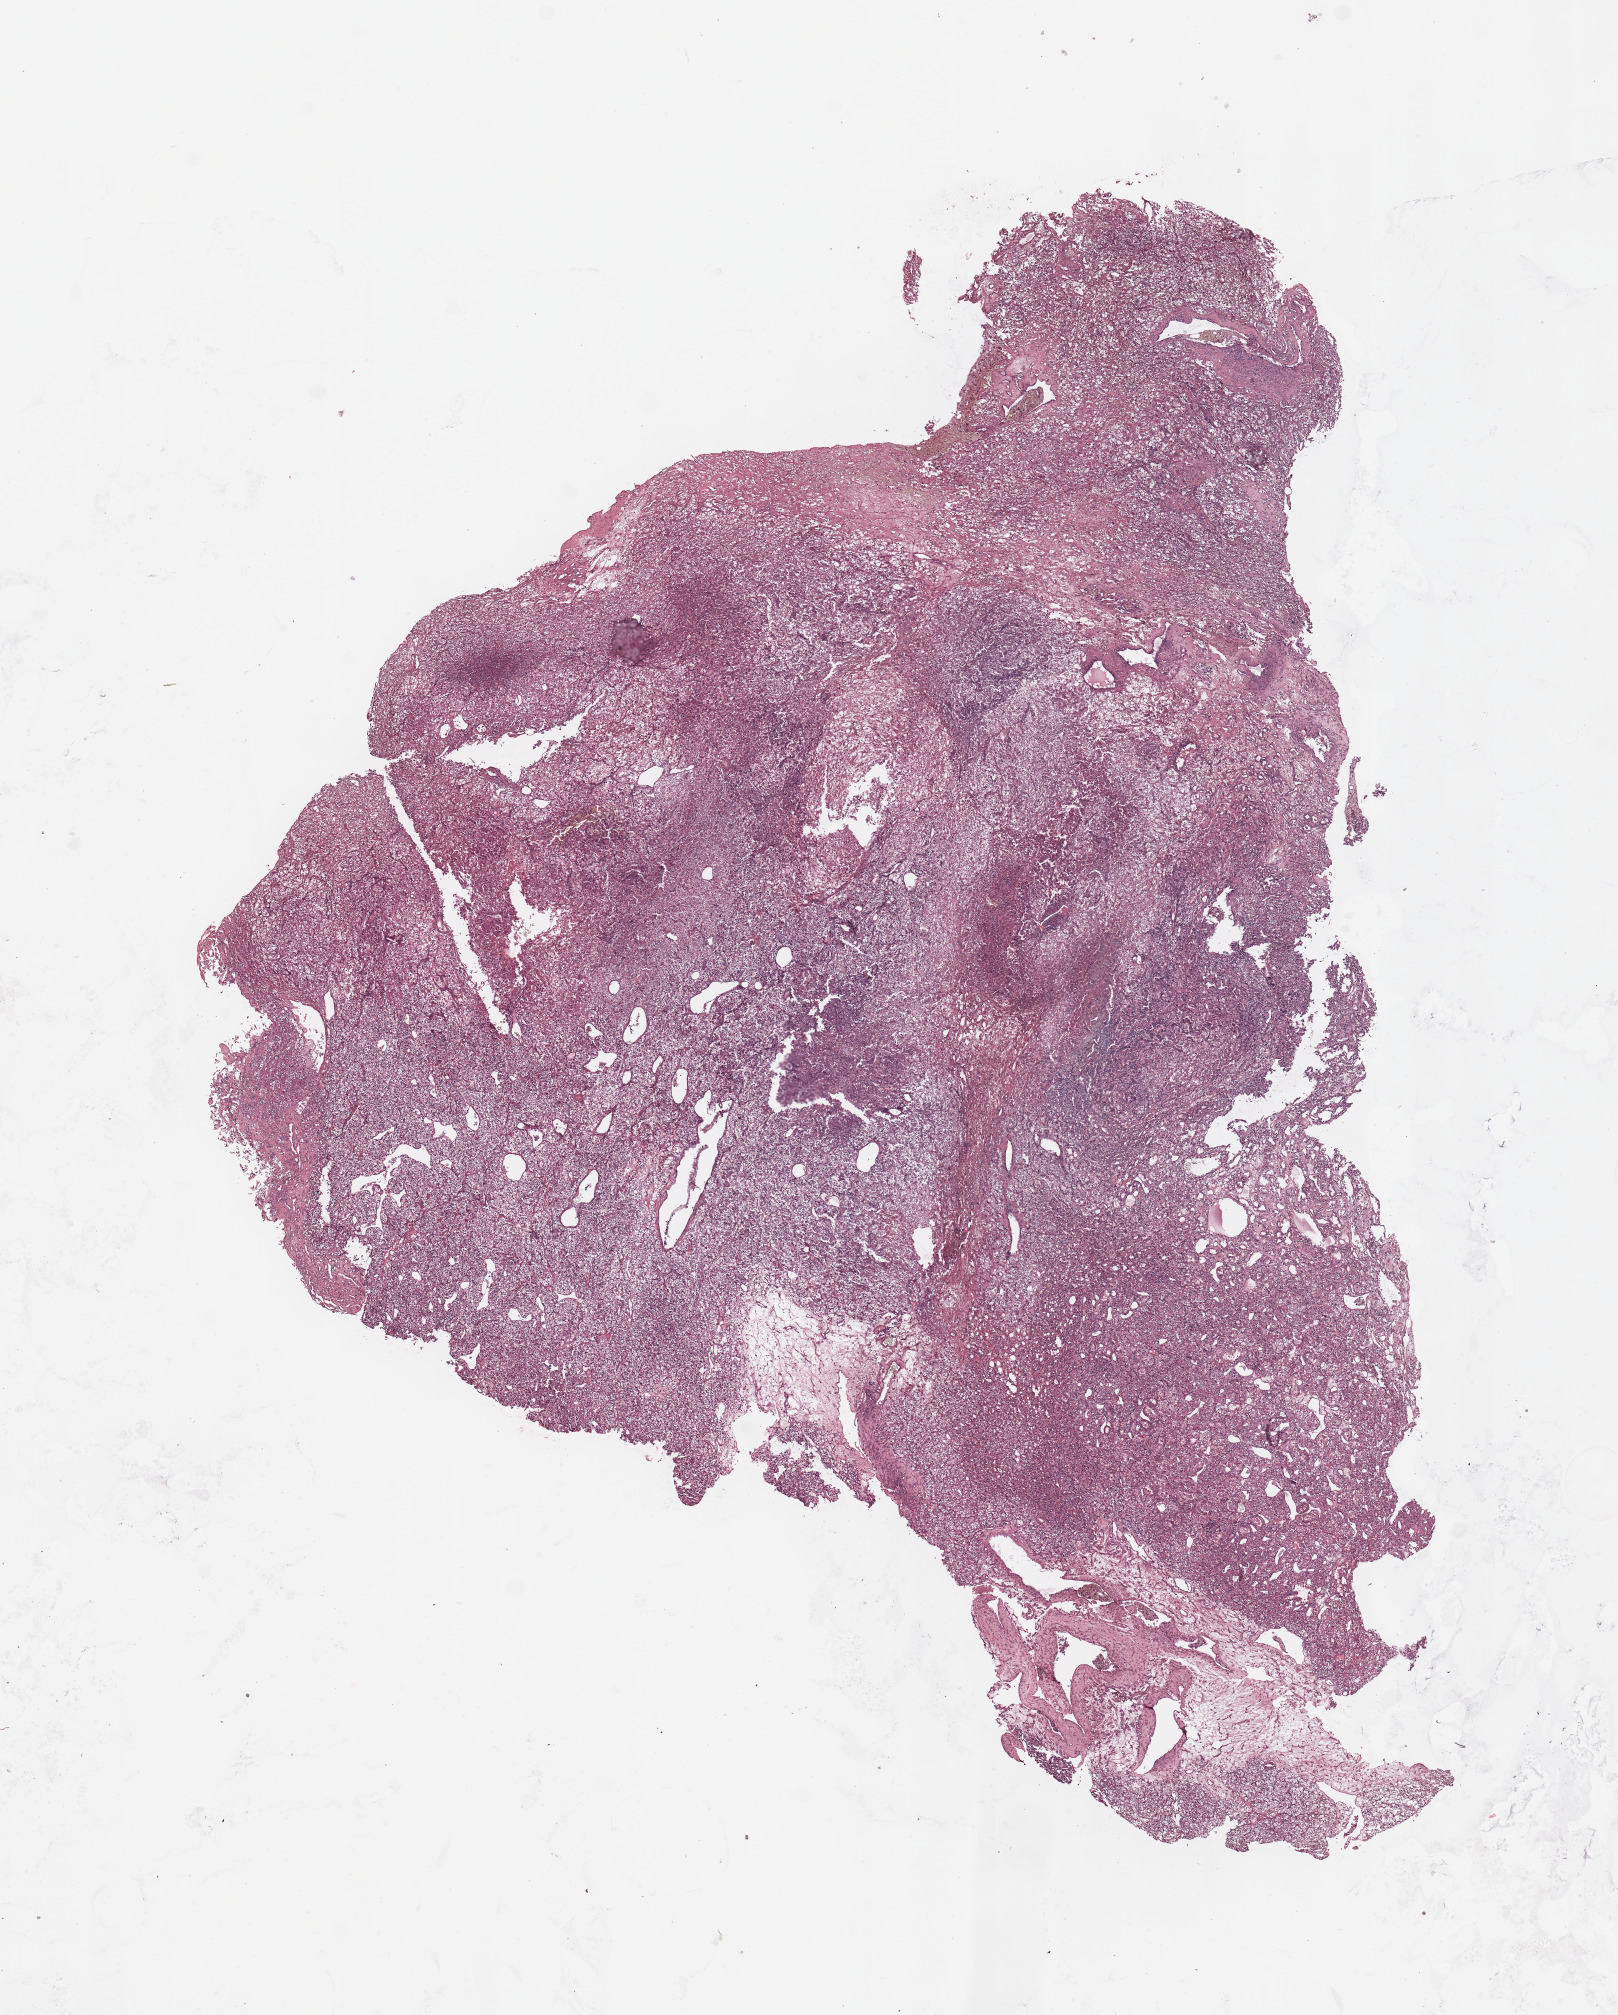
Digitized H&E tissue section (whole slide), a low-resolution overview of the entire scanned area, about 12.8 x 15.9 mm (from a 20x scan). Tumour tissue sample, sampled site: kidney. Male, 80 y/o. Histologic grade: G2 (moderately differentiated). Slide review estimates, as recorded: tumour nuclei 80%, necrosis 10%.
* primary tumour site (as recorded): upper pole
* diagnosis: Renal cell carcinoma, NOS
* AJCC pathologic stage: I